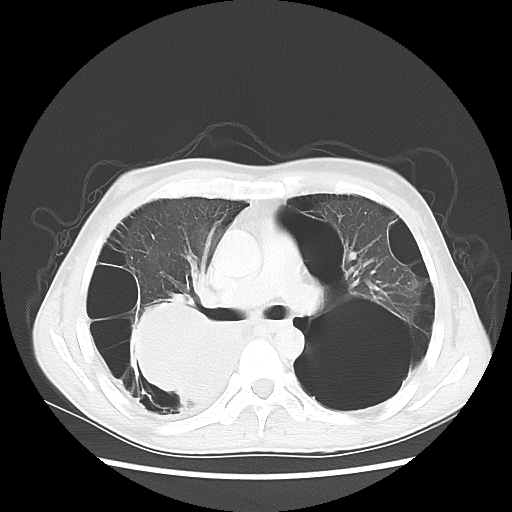
Chest CT, one axial slice; slice 34 of 57 in the series (ordered by position); lung window (W 1500 / L -600 HU); 5 mm slice thickness; 512 × 512 image matrix. Male patient, age 41 years. Case-level facts recorded for this patient, not image findings: clinical TNM (as recorded): T4 N0 M1a; histopathological grade: G3.
Annotated regions visible in this slice (bounding box drawn by a radiologist):
- lung tumour (recorded histology: large cell carcinoma): box from (x=134, y=298) to (x=254, y=407) px